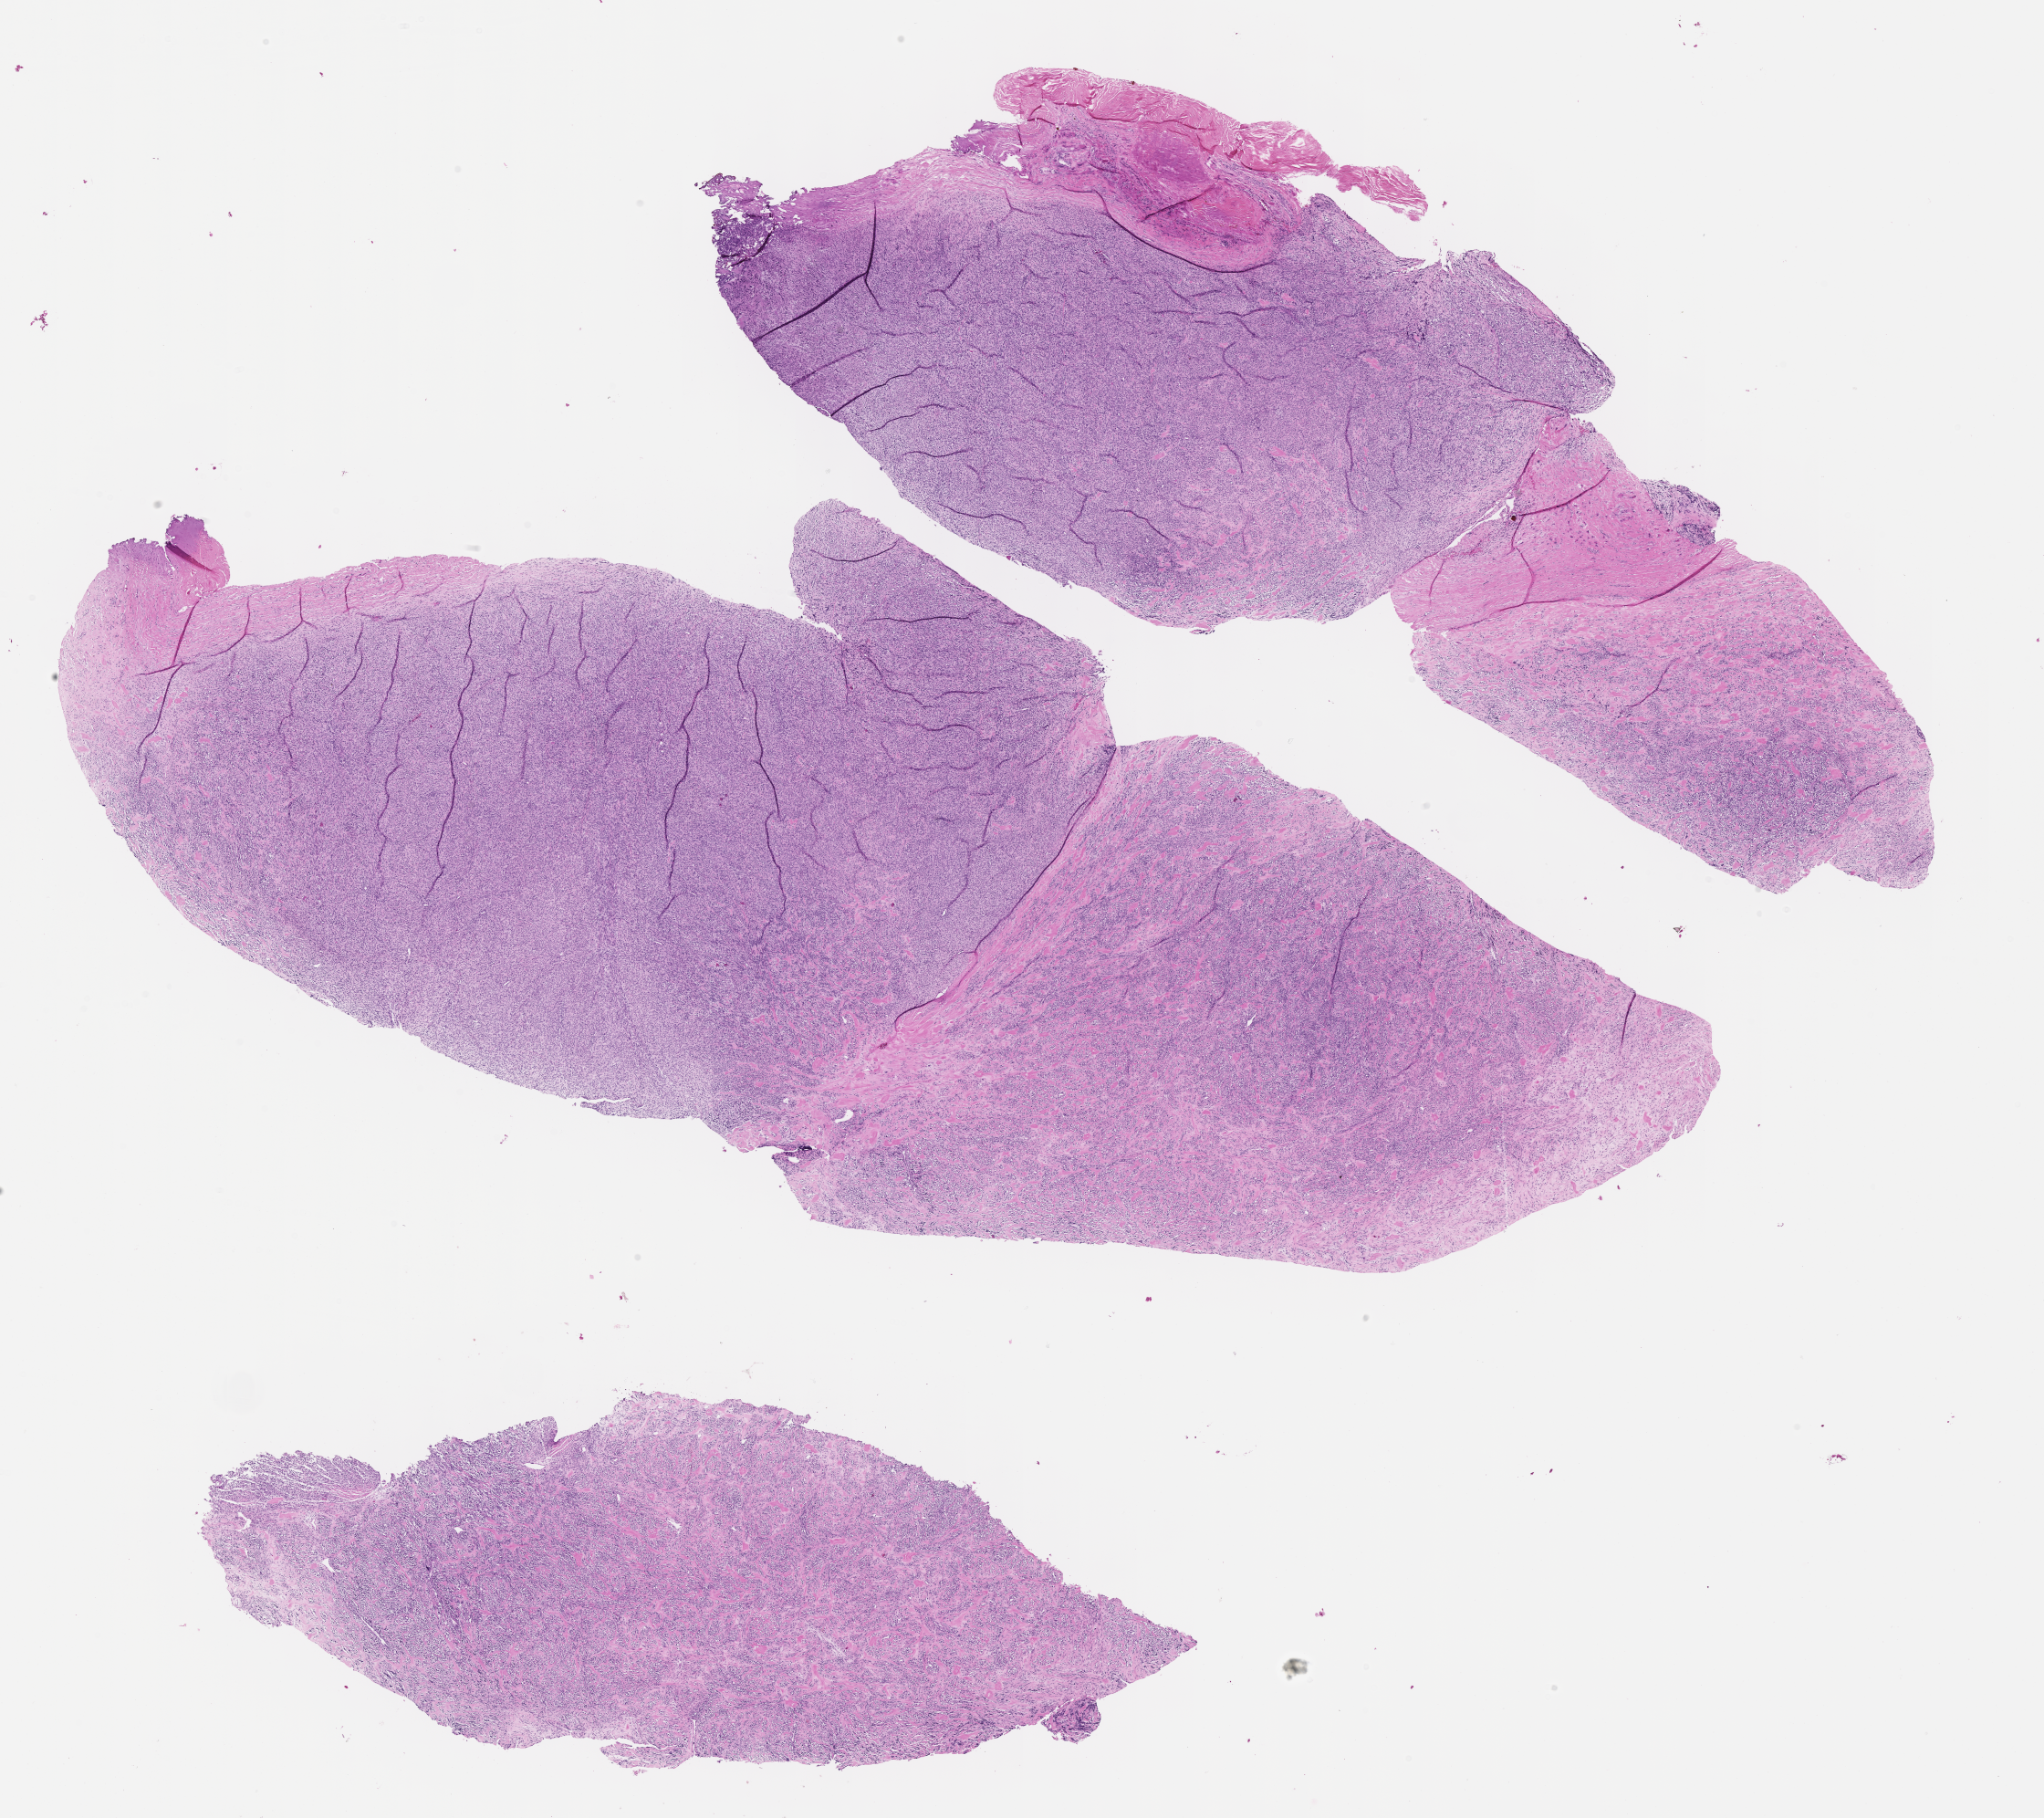
Haematoxylin and eosin whole-slide image of tumor tissue — low-resolution overview of the scanned area, about 18.1 x 16.1 mm, formalin-fixed paraffin-embedded section. Male patient, age at diagnosis 18.1 years.
- stage (as recorded): 3
- diagnosis: rhabdomyosarcoma; histological classification: spindle cell rhabdomyosarcoma